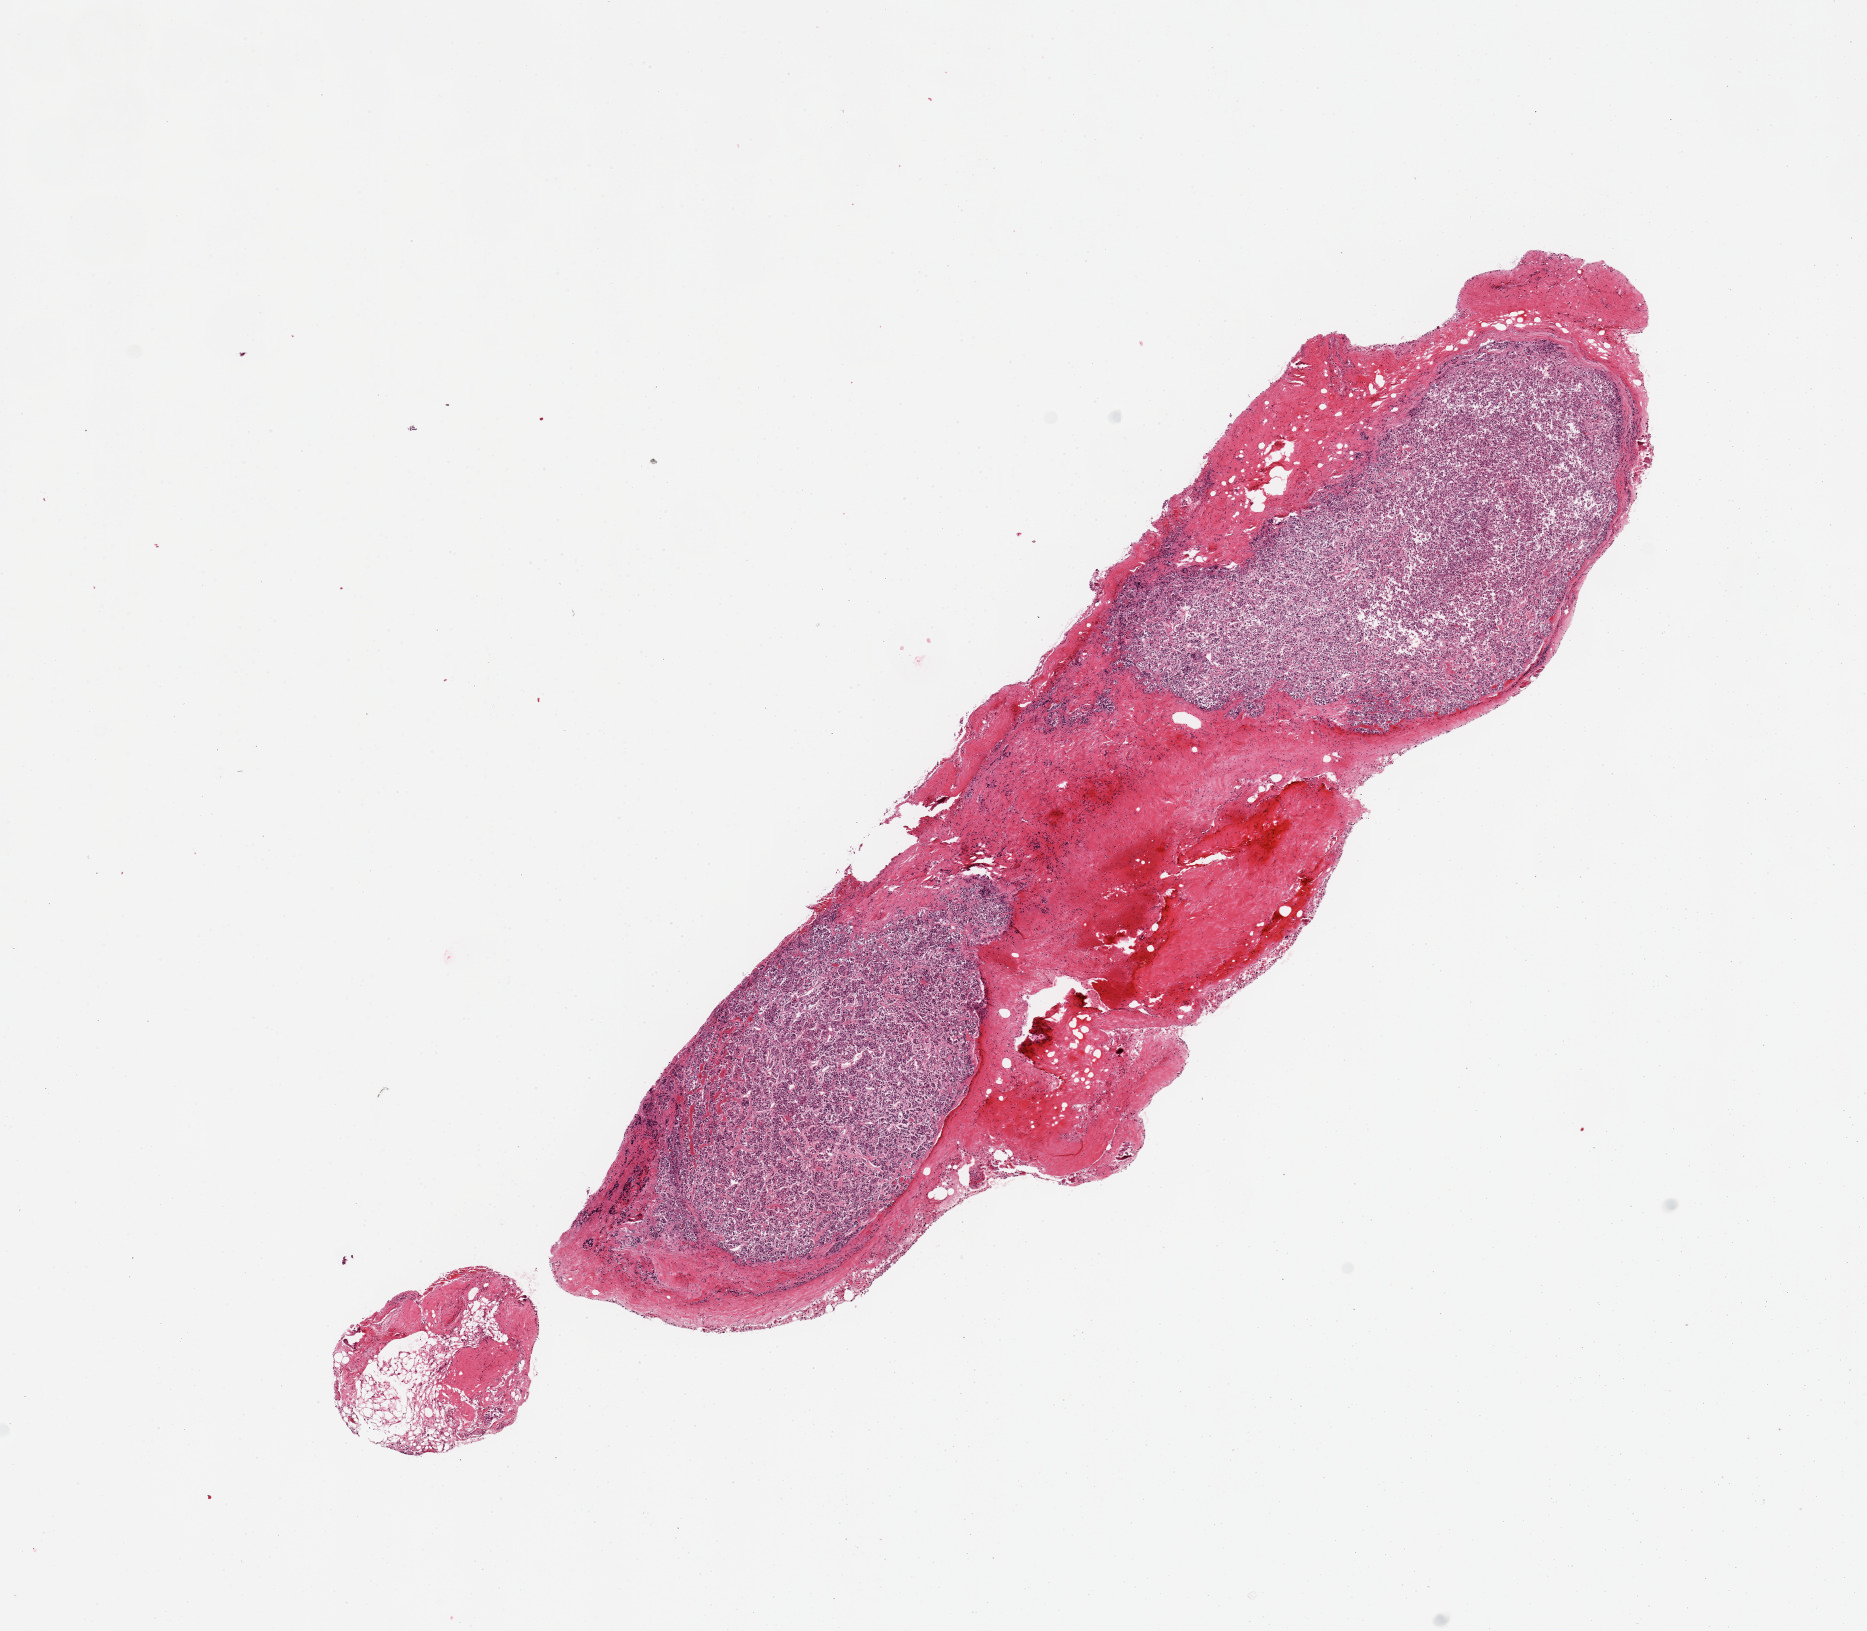
Digitized H&E-stained section — low-resolution overview of the scanned area, about 14.8 x 12.9 mm (from a 20x scan); PAXgene-fixed, paraffin-embedded tissue; sampled site (target tissue): pituitary; donor tissue sample.
- review note (as recorded): 2 pieces; anterior gland with 30% fibrous capsule